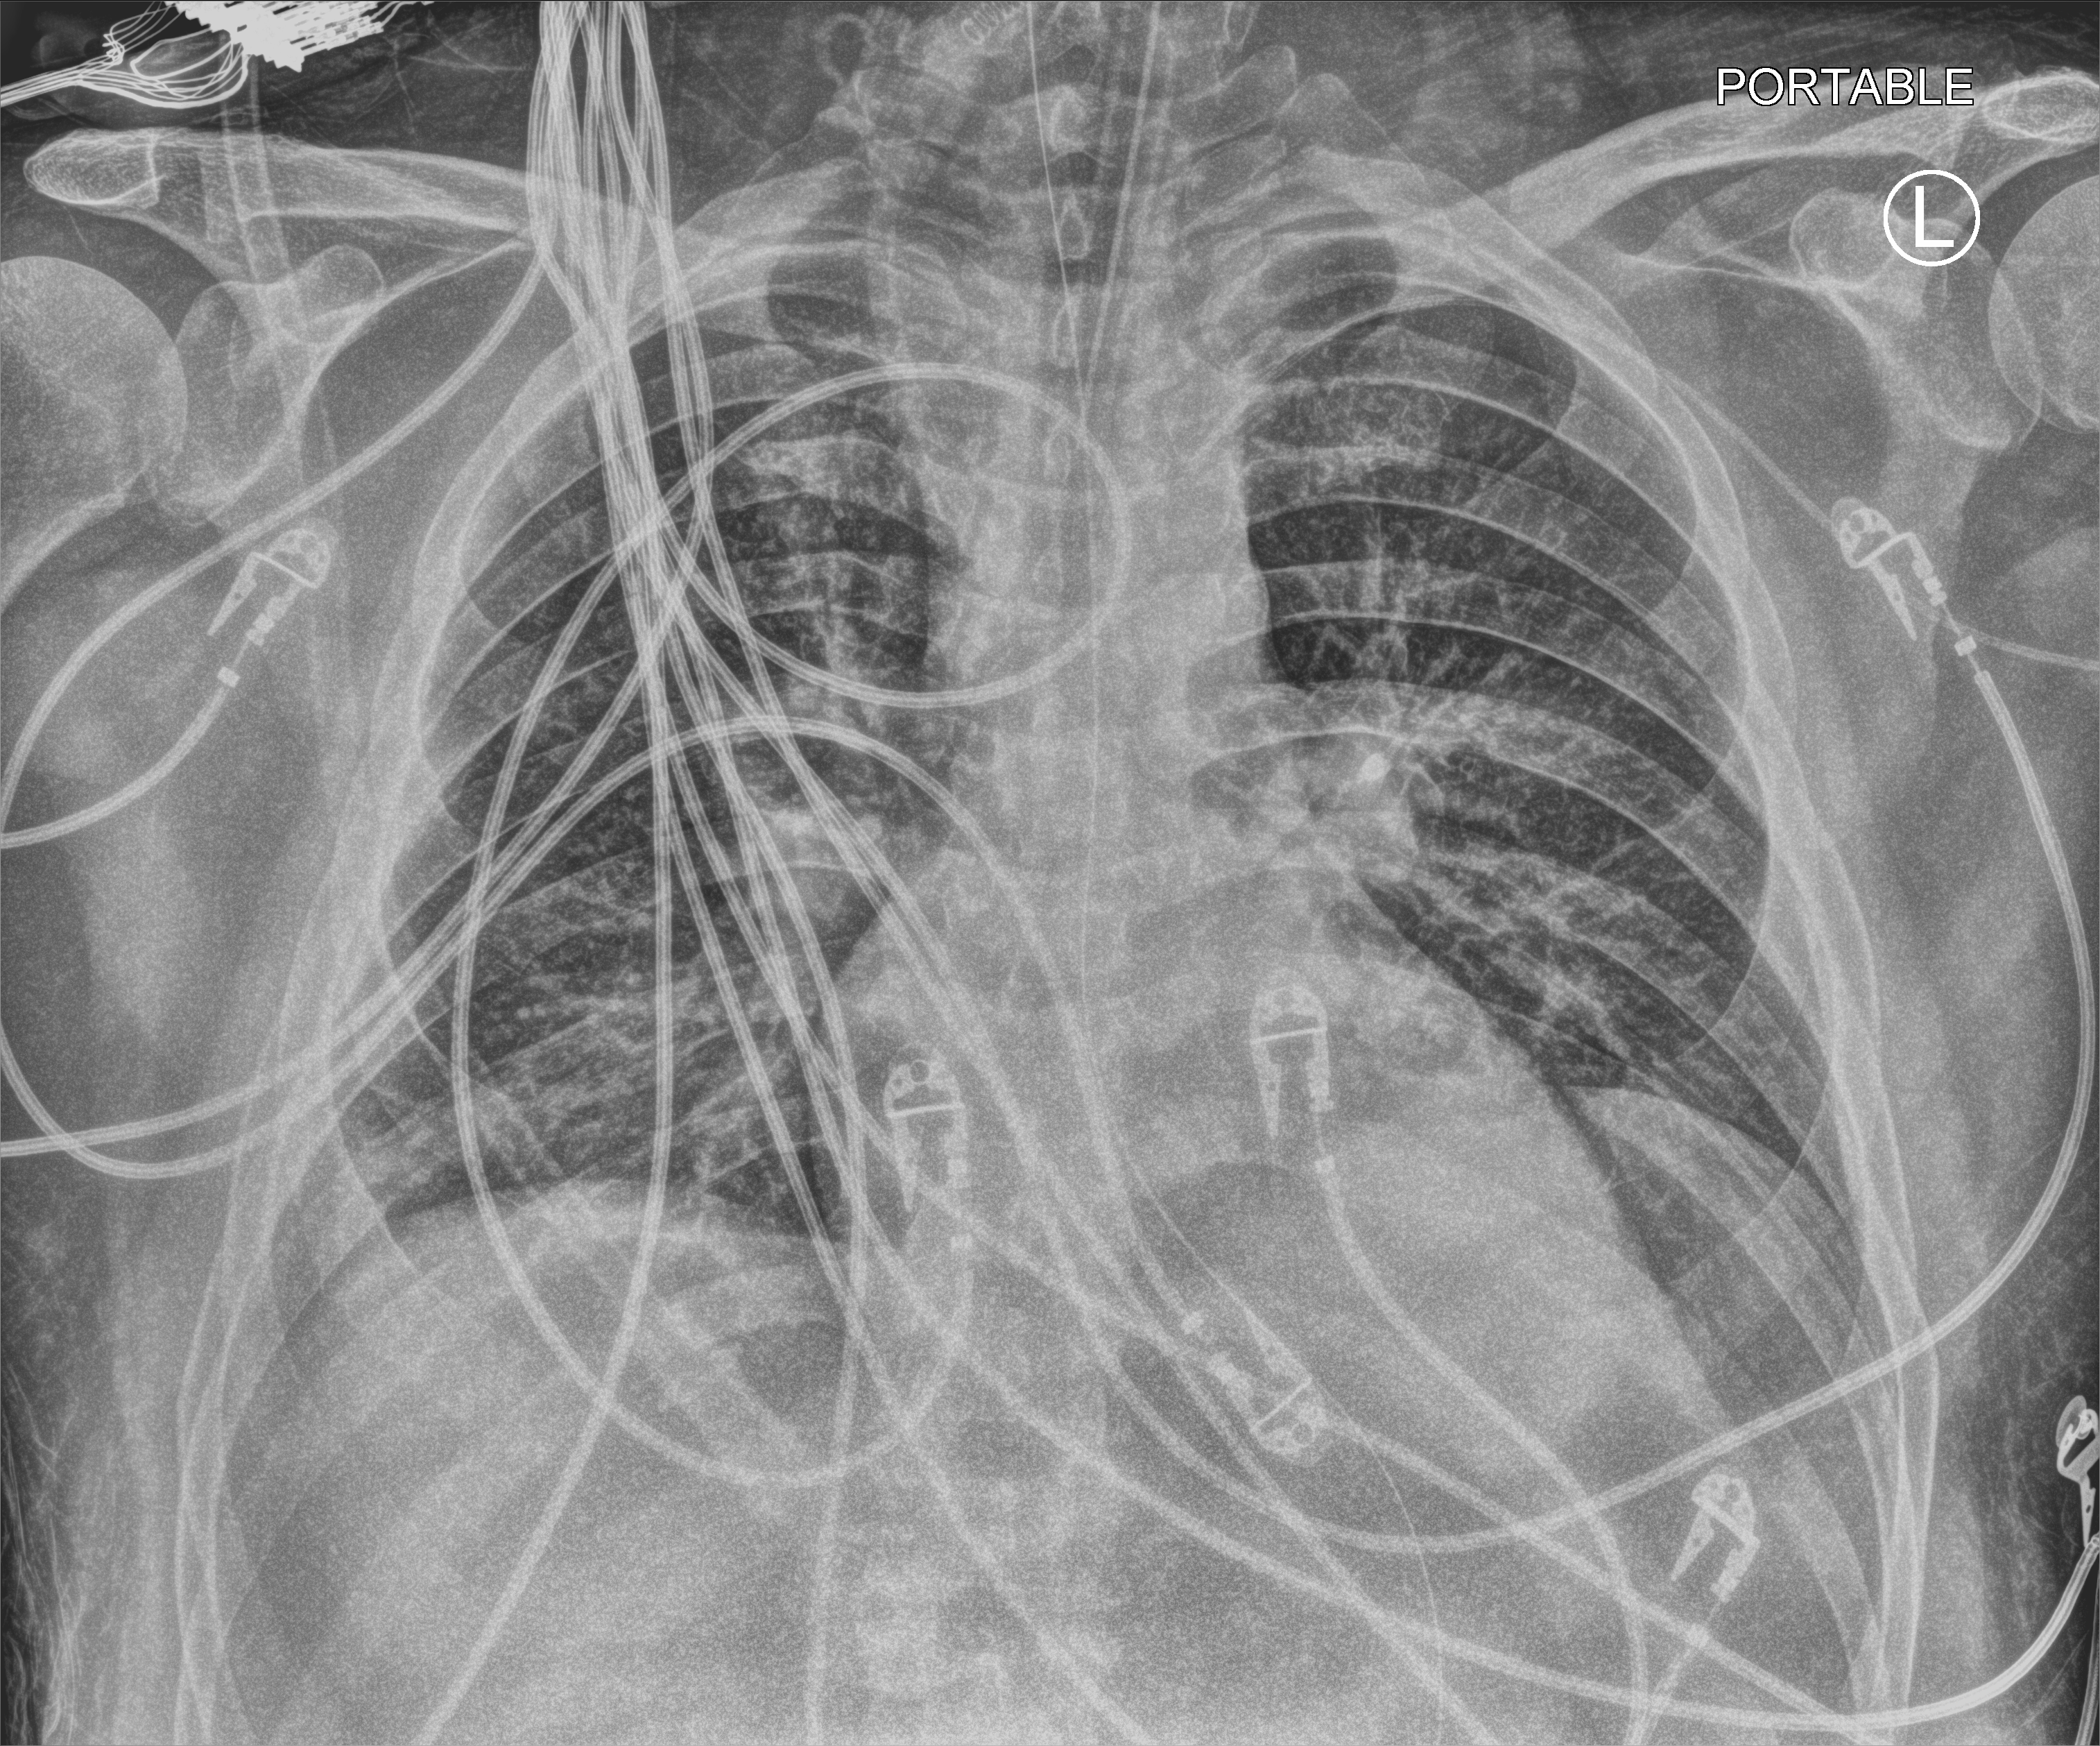
Chest X-ray (portable). Patient hospitalised with COVID-19; male, aged 18–59 years.
From the hospital-stay record, not from the radiograph (when in the stay this image was taken is not recorded): mechanically ventilated during this hospital stay: yes.